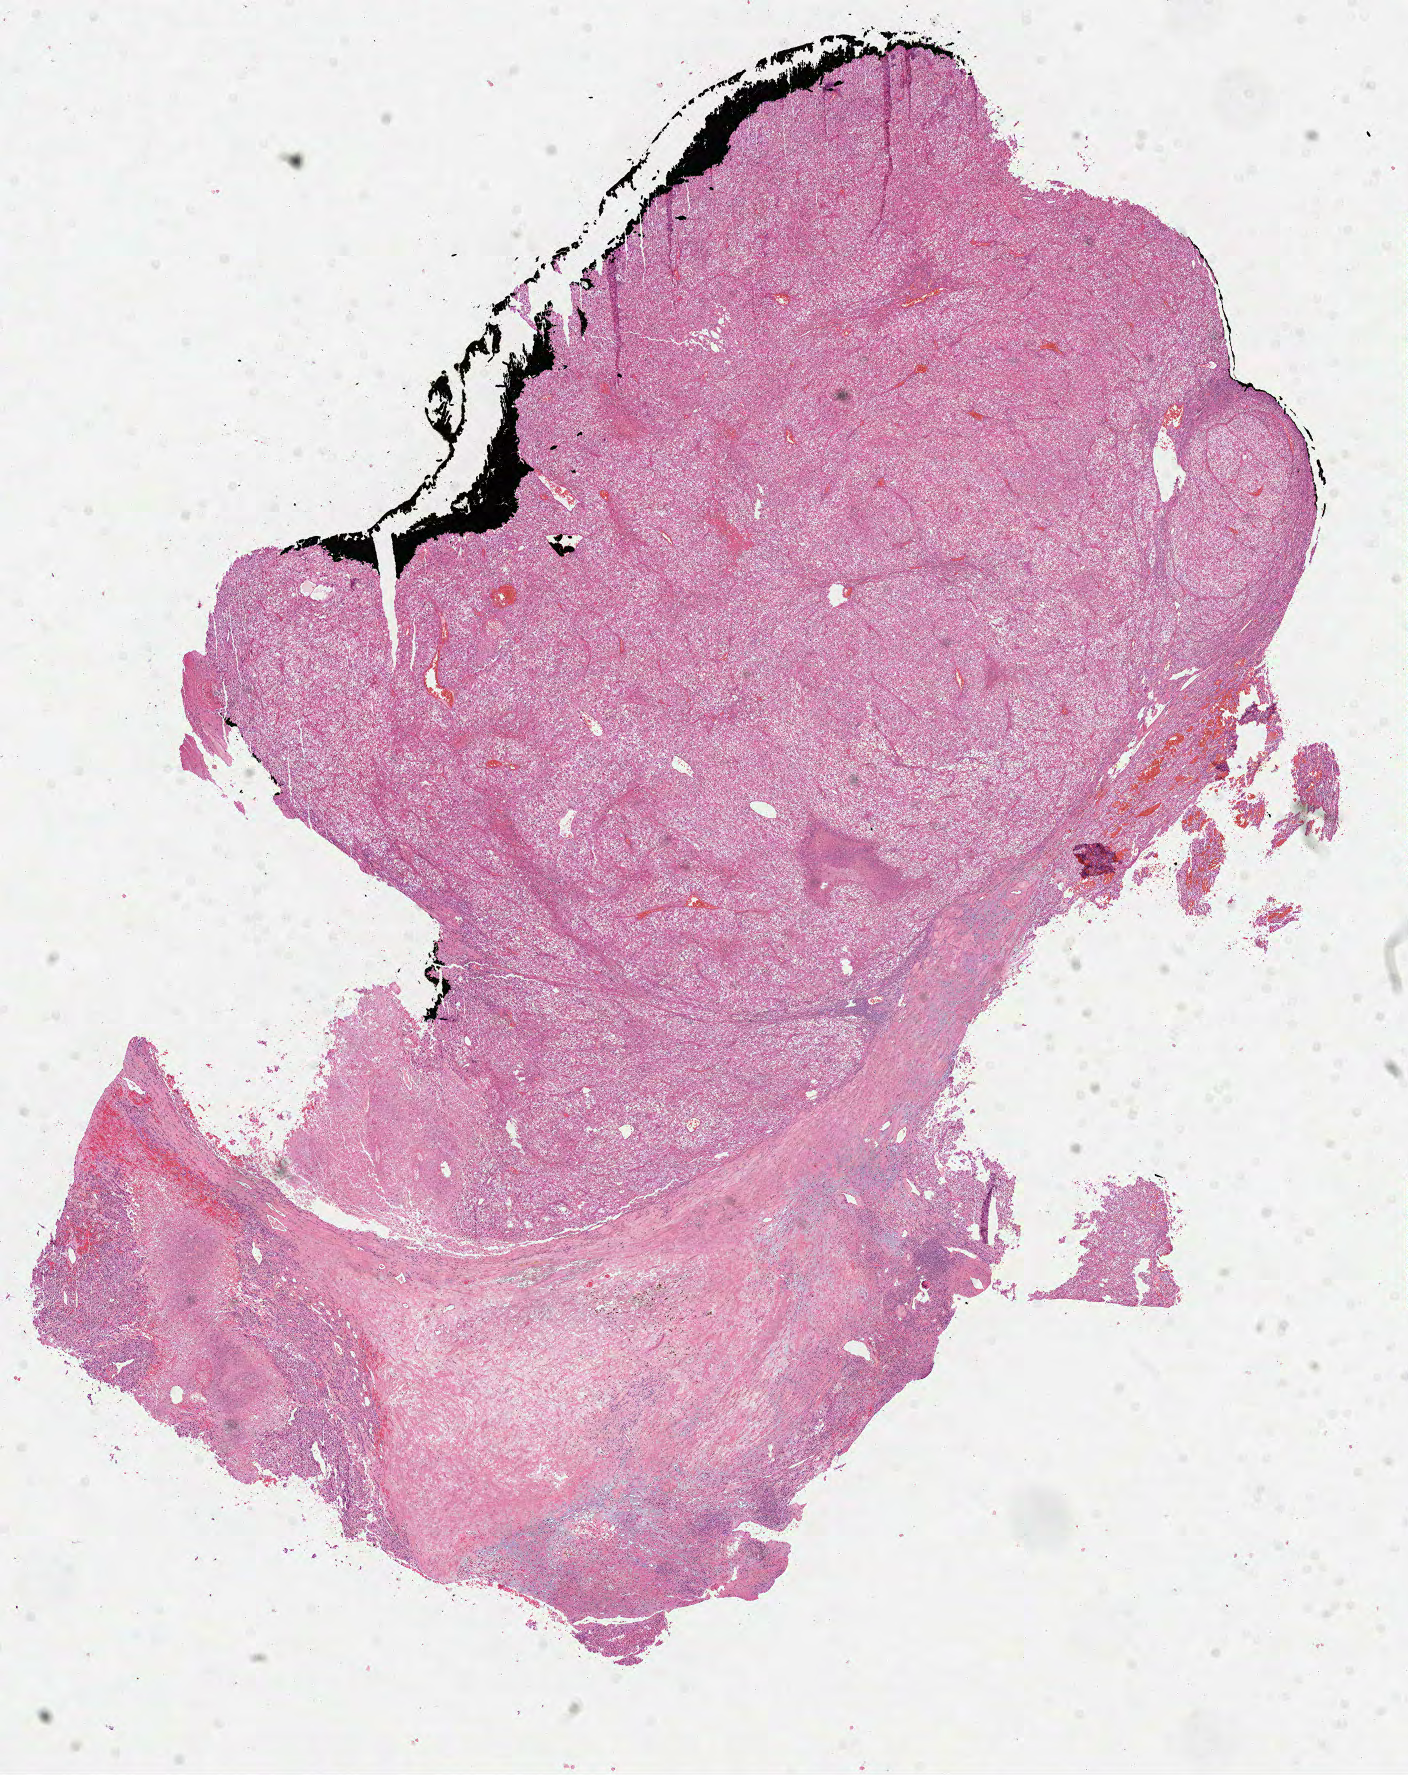
Whole-slide histology image, H&E — low-resolution overview of the scanned area, about 11.4 x 14.3 mm (from a 40x scan). Formalin-fixed paraffin-embedded (FFPE) diagnostic section. Primary tumour sample from the kidney. Patient: male, age at initial diagnosis 70 years. Histologic grade: G2 (moderately differentiated).
- AJCC pathologic stage: I
- histologic diagnosis: Clear cell adenocarcinoma, NOS